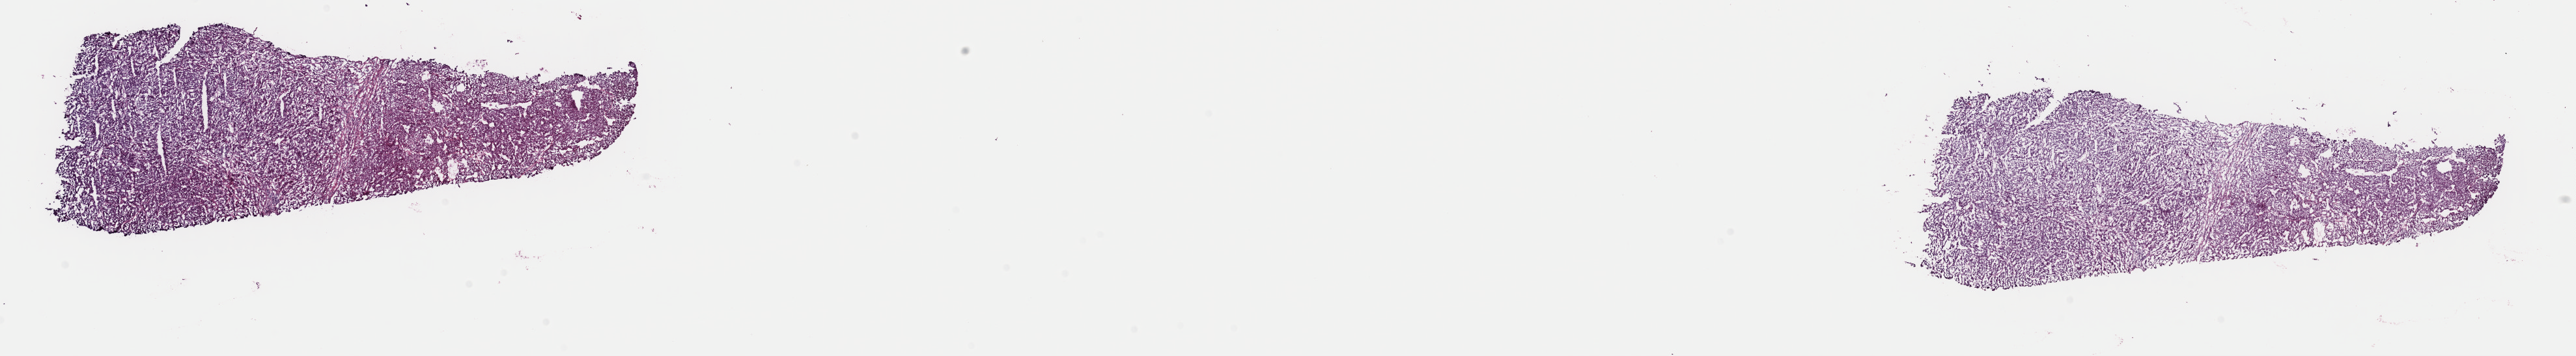
H&E whole-slide image, a low-resolution overview of the entire scanned area, about 31.2 x 4.3 mm (from a 40x scan). Frozen section from the top of the tissue portion. Primary tumour sample from the liver. Male patient; age at initial diagnosis 57 years. Histologic grade: G1 (well differentiated). Composition of this section per pathologist review: tumour cells 100%, tumour nuclei 80%, normal cells 0%, stromal cells 0%, necrosis 0%. Infiltration values recorded for this section: lymphocyte infiltration 1%, monocyte infiltration 0%, neutrophil infiltration 0%.
Histologic diagnosis: Hepatocellular carcinoma, NOS. AJCC pathologic stage: I (7th edition).